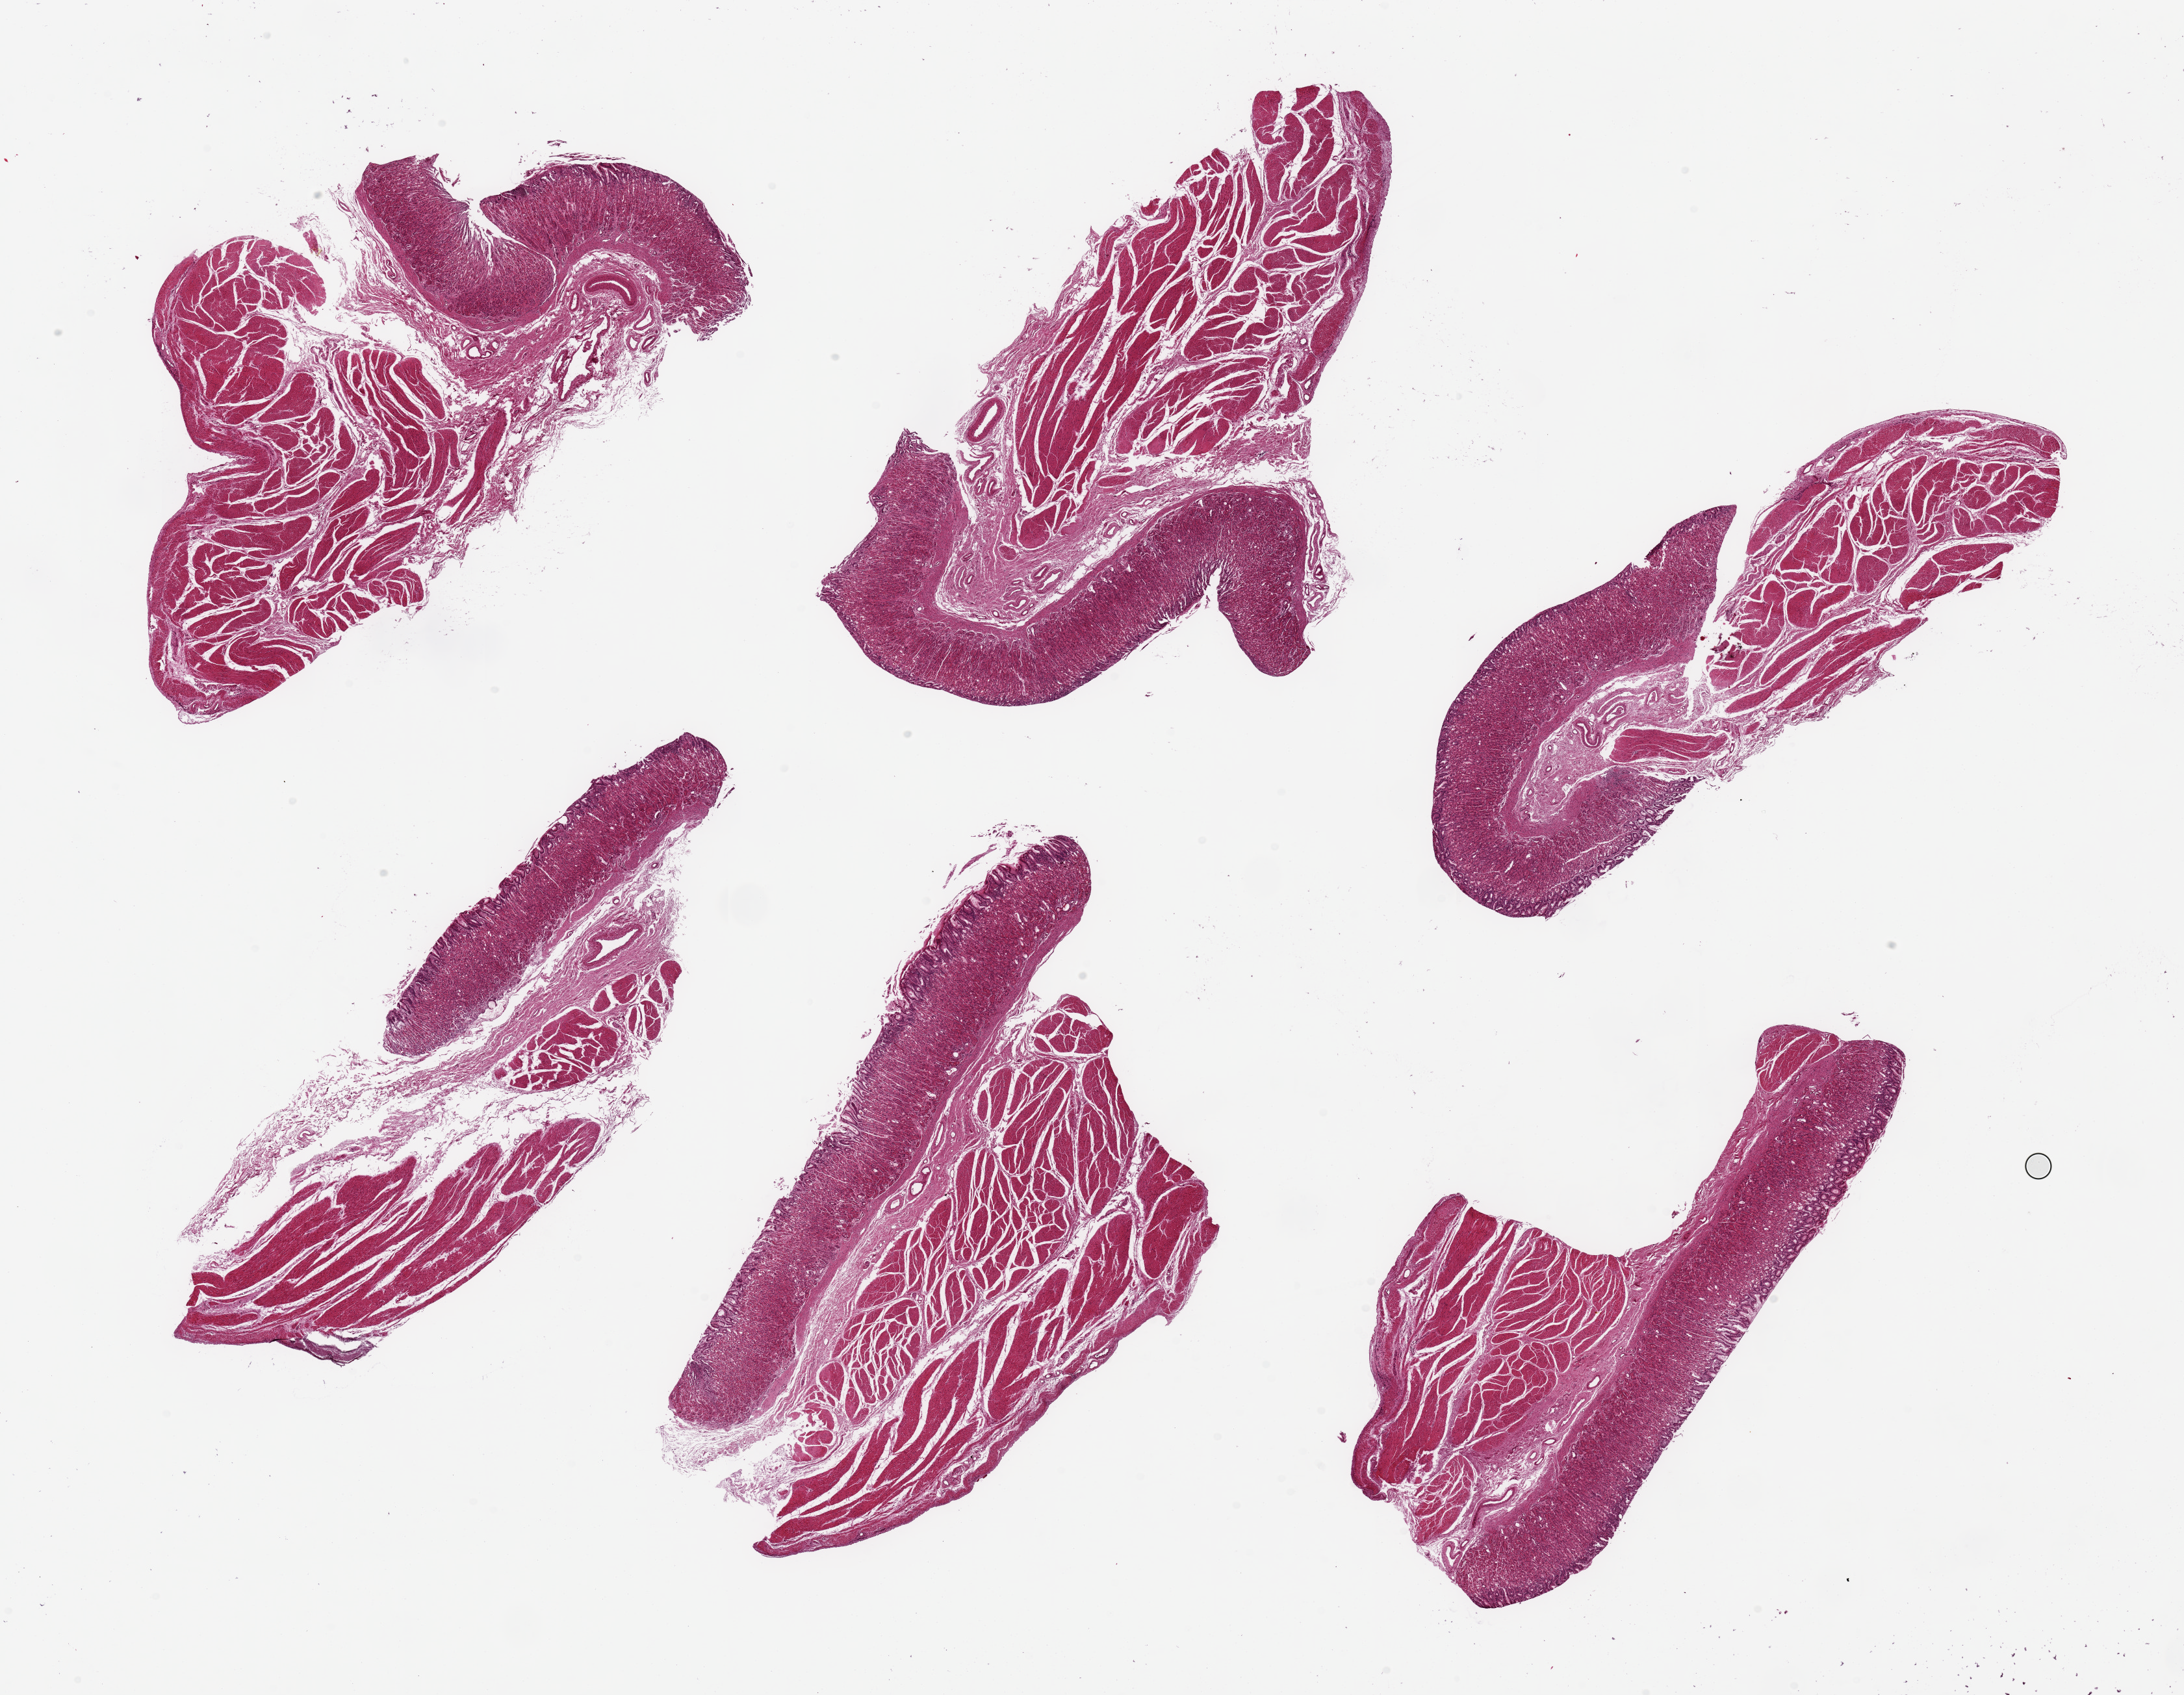
Digitized H&E-stained section — a low-resolution overview of the entire scanned area, about 26.6 x 20.6 mm (from a 20x scan); PAXgene-fixed paraffin-embedded (PFPE) section; target tissue: stomach; tissue donor sample. Female donor.
Reviewer comment on this tissue sample: 6 pieces up to 8x5 mm; mucosa ~ 1mm. good preservation.